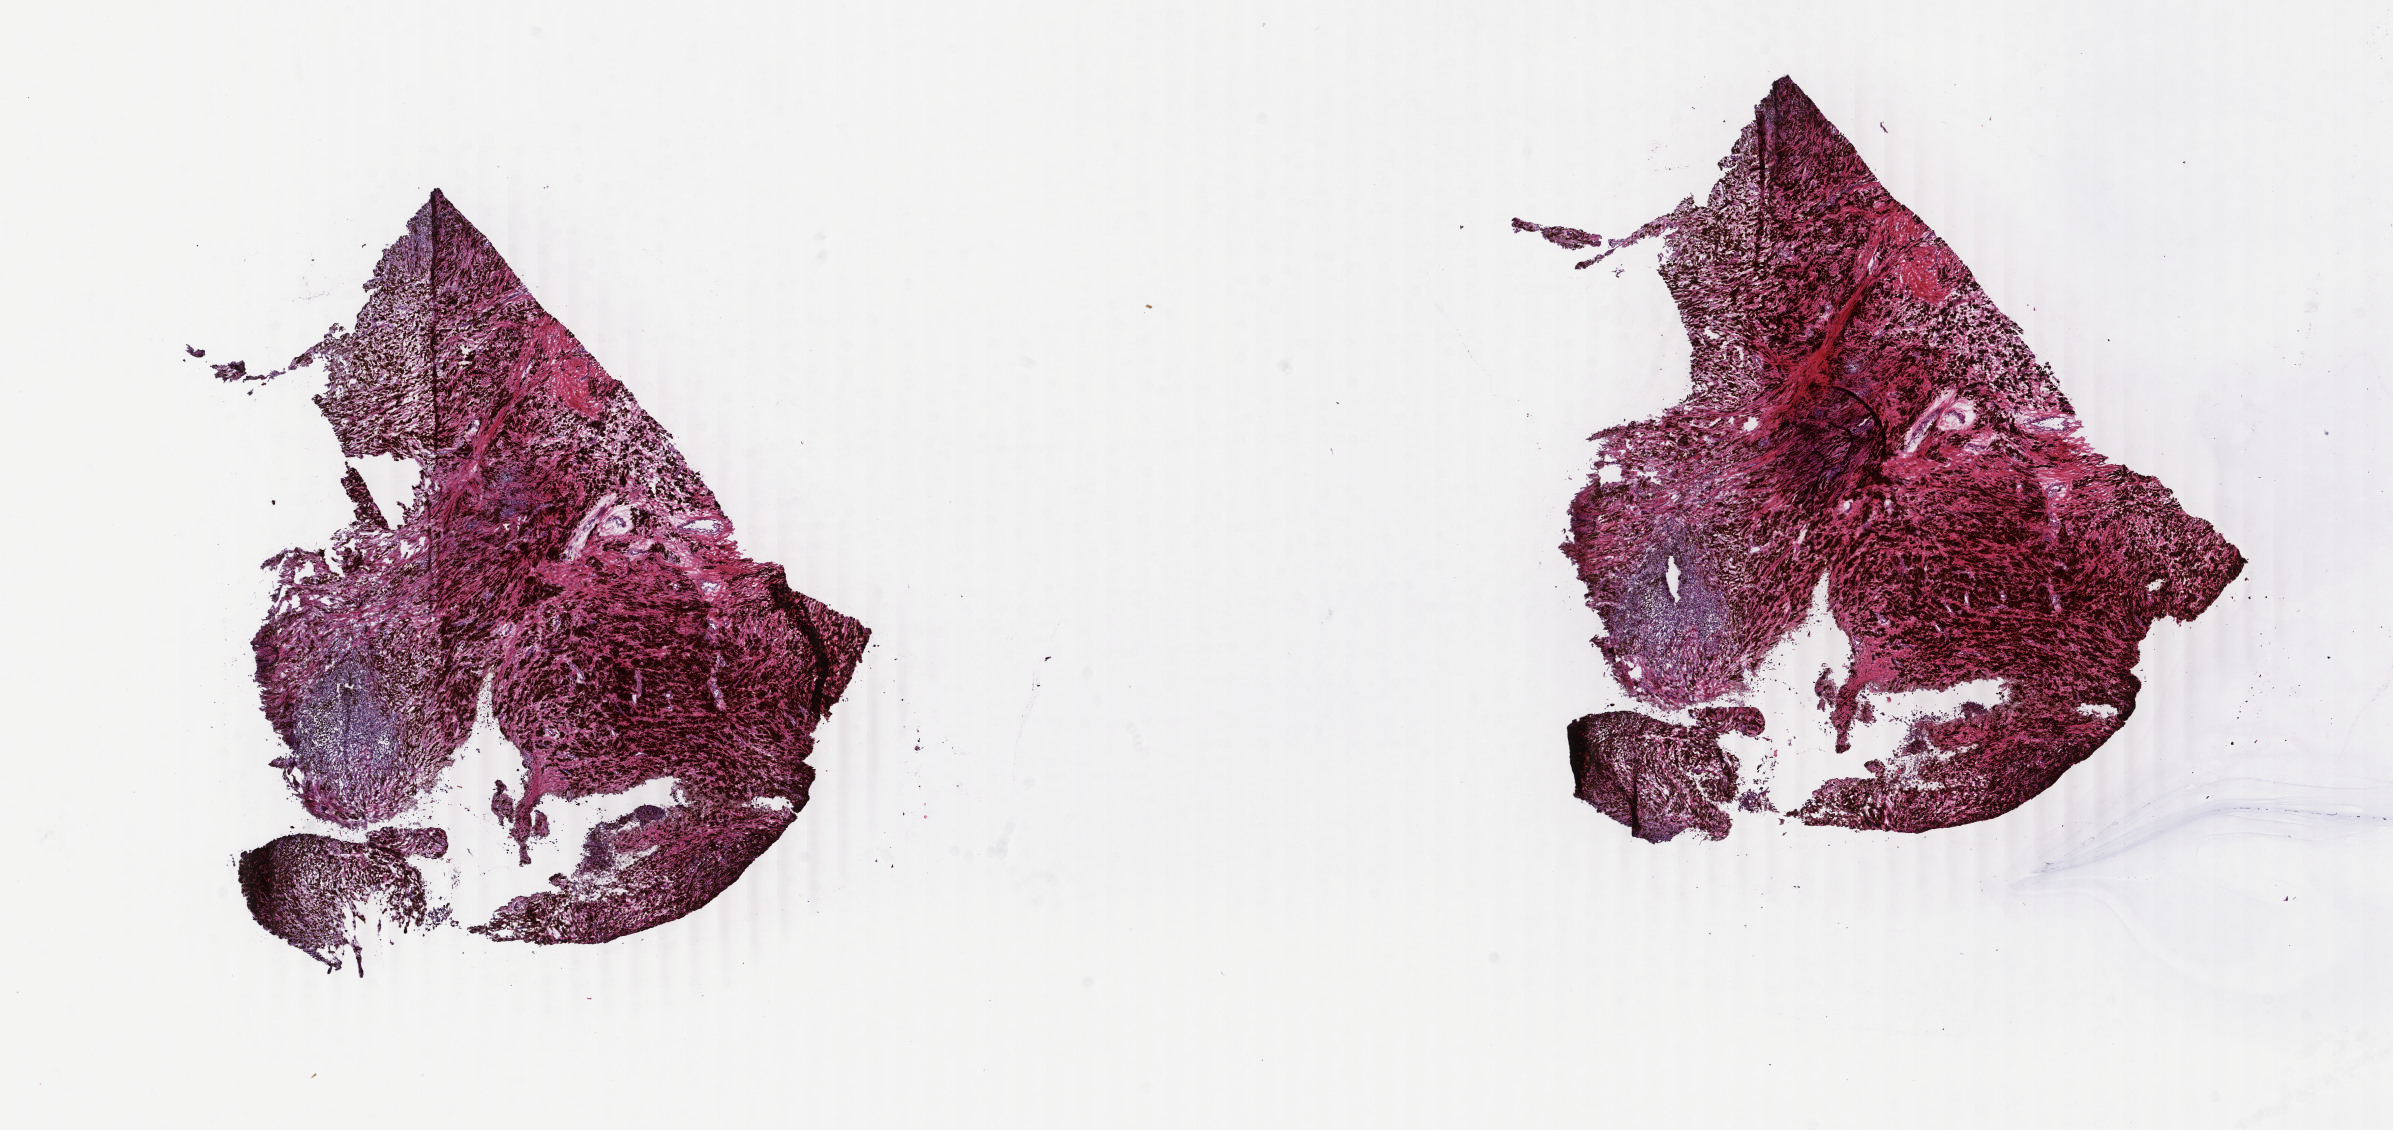
H&E whole-slide image — a low-resolution overview of the entire scanned area, about 19.0 x 9.0 mm (acquisition: 40x scan). Frozen section. Sample: primary tumour, skin. Male patient; age at initial diagnosis 77 years. Slide review estimates, as recorded: tumour cells 100%, tumour nuclei 80%, normal cells 0%, stromal cells 0%, necrosis 0%. Inflammatory infiltration, as recorded: lymphocyte infiltration 0%, monocyte infiltration 0%, neutrophil infiltration 0%.
Histologic diagnosis: Malignant melanoma, NOS.